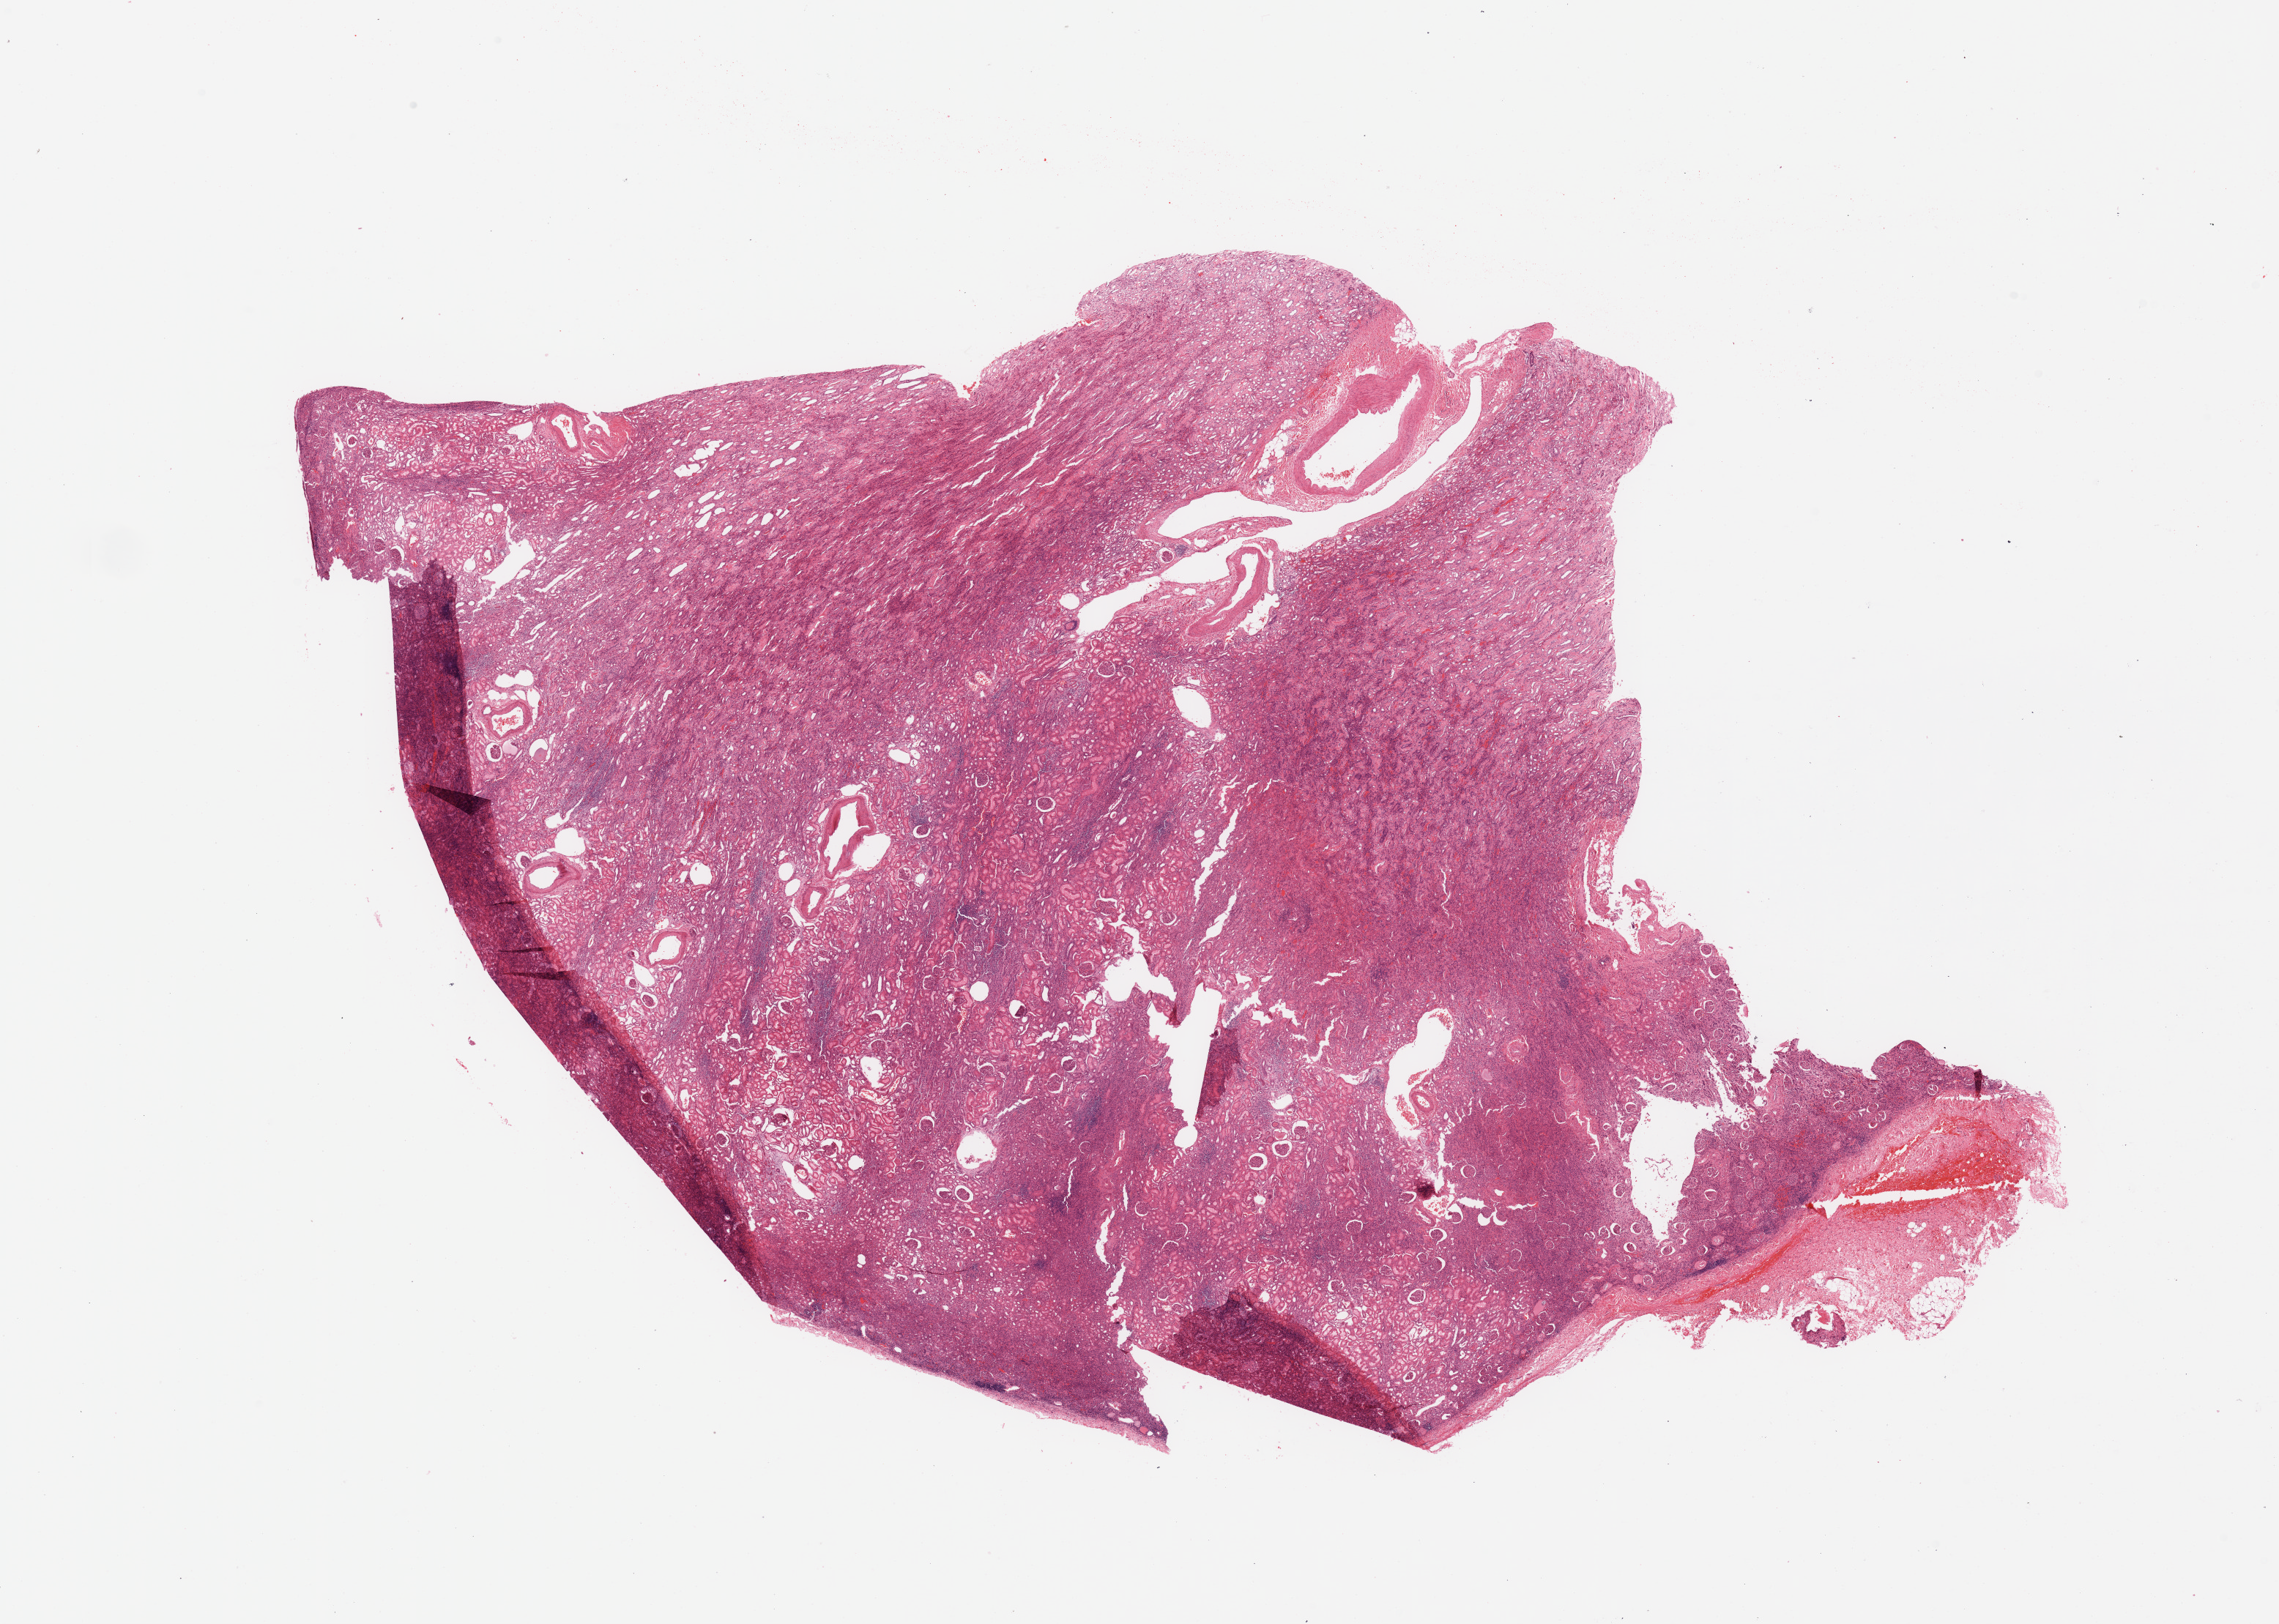
H&E-stained whole-slide image — shown as a low-resolution overview of the whole scanned area (about 24.6 x 17.5 mm); kidney, normal (non-tumour) tissue. Patient: female, age 68 years.
This section: normal (non-tumour) tissue from the same patient. Patient diagnosis: Renal cell carcinoma, NOS.